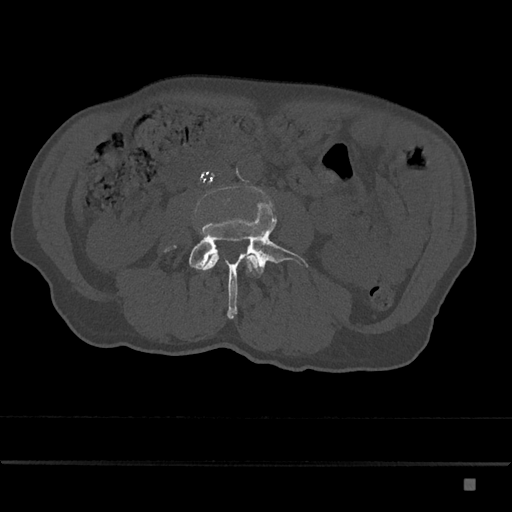
CT including the spine, one axial slice. Position 358 of 797 along the scan axis. Reconstruction kernel Br40s/3. 120 kVp. Bone window (W 1800 / L 400 HU). 0.5 mm slice thickness. 512 × 512 image matrix. Male patient, age 72 years. From the clinical record (not read from this slice): primary cancer: prostate.
Outlined on this slice (semi-automatic segmentation, software-assisted and operator-edited):
- L3 vertebra: bounding box <203,253,259,271> (left, top, right, bottom; pixels)
- L4 vertebra: <164,202,309,319>